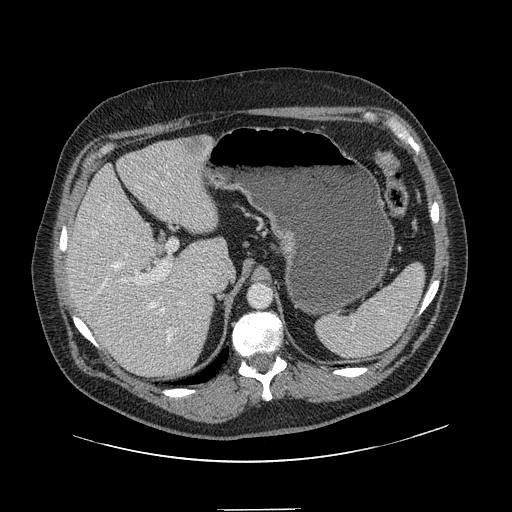
Contrast-enhanced abdominal CT, one axial slice. Slice 98 of 154 in the series (ordered by position). Intravenous contrast given. Soft-tissue window (W 400 / L 40 HU). 512 × 512 image matrix, field of view 451 × 451 mm. Male patient, age 61 years. From the clinical record (not read from this slice): diagnosis: colorectal cancer liver metastases, imaged before liver resection; multiple liver metastases: yes; largest metastasis: 2.6 cm; disease in both lobes: yes.
Annotated regions visible in this slice (outlined manually by an expert reader):
- hepatic veins: bounding box <92,215,177,345> (left, top, right, bottom; pixels)
- liver: <68,137,226,379>
- planned liver remnant (the part of the liver to remain after resection): <68,145,225,363>
- portal vein (with intrahepatic branches): <108,167,186,305>
- liver metastasis: <185,140,205,158>